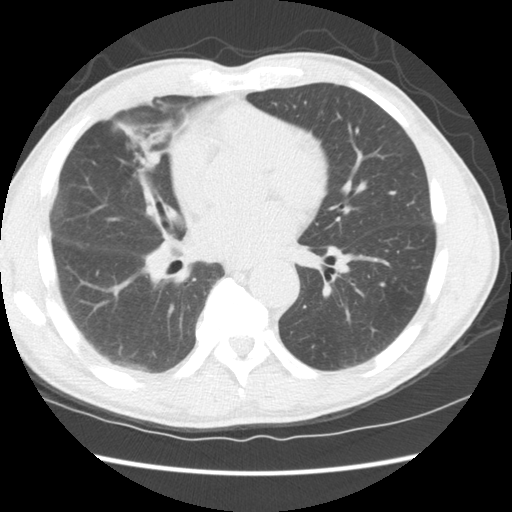
Low-dose screening chest CT, one axial slice; slice 67 of 147 in the series (ordered by position); 120 kVp; lung window (W 1500 / L -600 HU); 2.5 mm slice thickness; 512 × 512 image matrix, field of view 345 × 345 mm.
Outlined on this slice (outlined manually by an expert reader):
- lesion 1 (tumor, middle lobe of right lung): box from (x=145, y=149) to (x=160, y=168) px